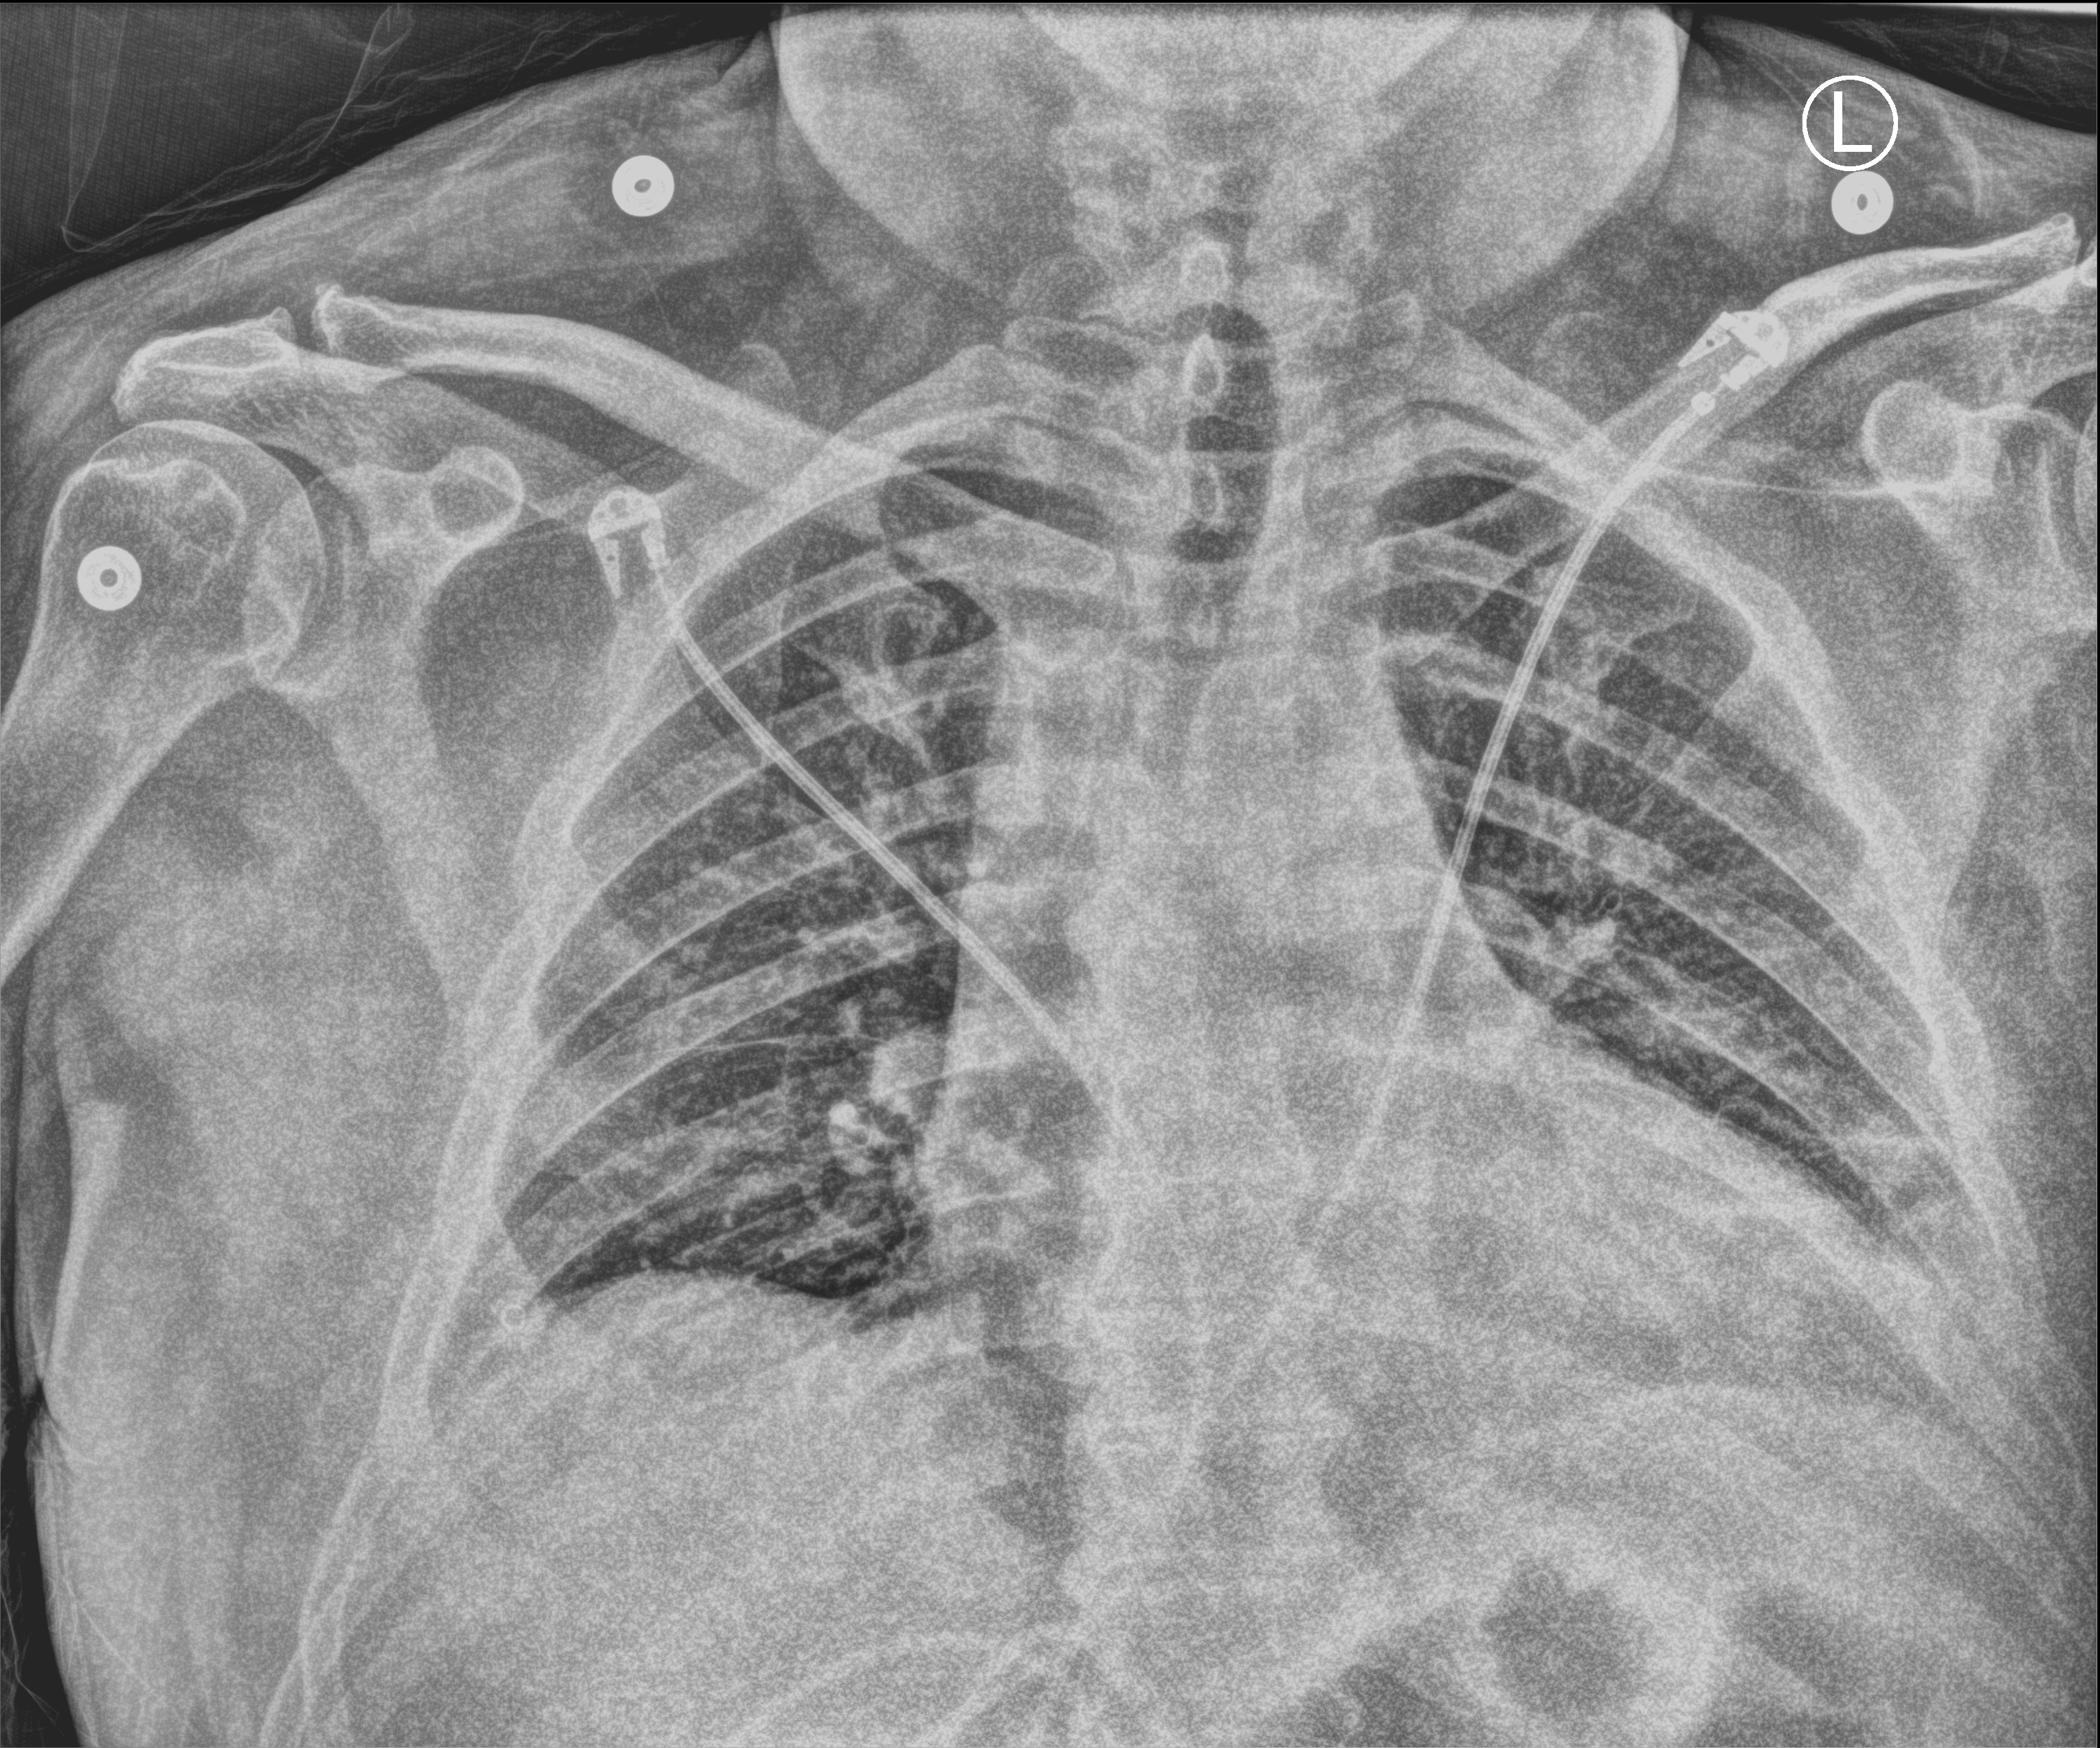
Bedside chest radiograph (computed radiography). Male patient hospitalised with COVID-19, age 18–59 years.
Hospital-stay facts (about this admission, not read from this image; timing relative to this image not recorded): length of hospital stay: 10 days; mechanically ventilated during this hospital stay: no; admitted to intensive care during this hospital stay: no.